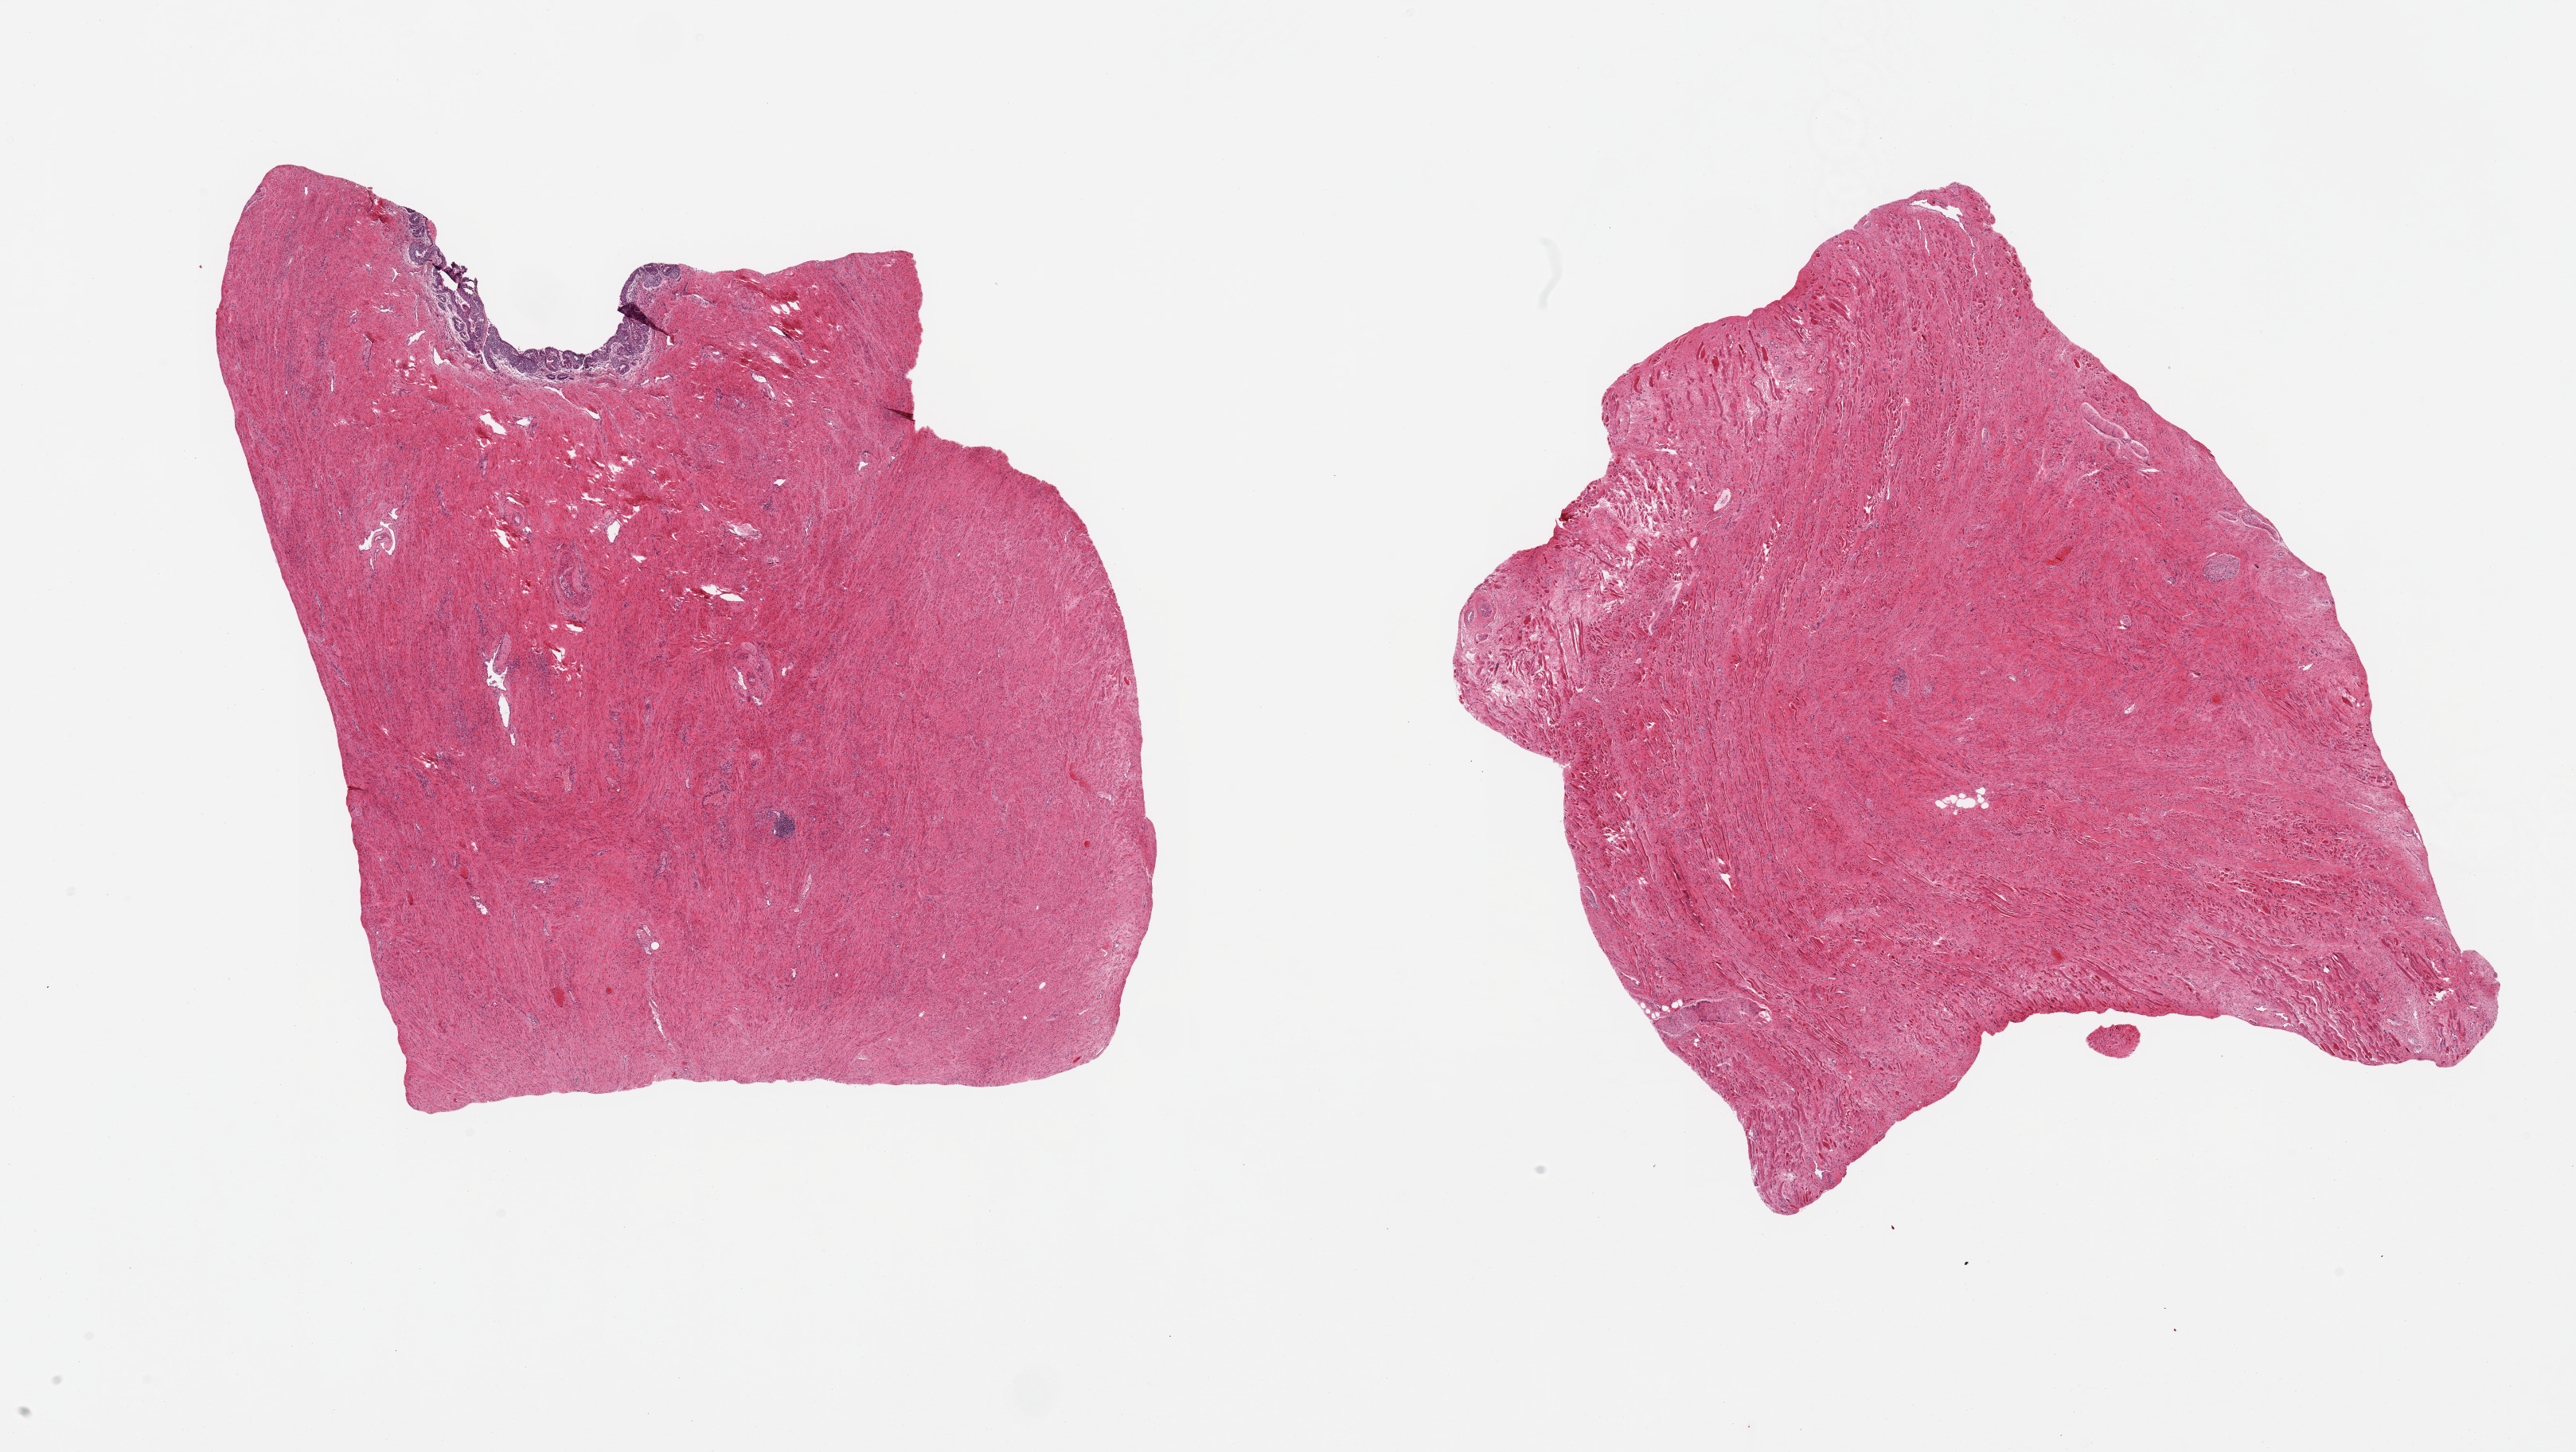
H&E whole-slide image, brightfield, a low-resolution overview of the entire scanned area, about 25.6 x 14.4 mm (acquisition: 20x scan), PAXgene-fixed paraffin-embedded (PFPE) section, target tissue: prostate, donor tissue sample. Donor sex: male.
Review note (as recorded): 2 pieces; all fibromuscular stroma, no glands; 1 has band of urethral mucosa on 1 side; other piece has one end with admixed skeletal muscle.